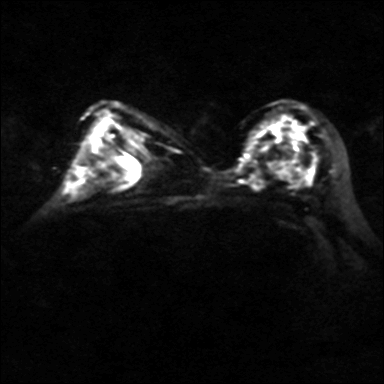
Breast MRI, one axial slice; position 24 of 40 along the scan axis; diffusion-weighted series; image 2 of 4 stored at this slice position (different b-values; order by instance number); 3 T; 4 mm slice thickness; 384 × 384 image matrix, field of view 320 × 320 mm. Female patient.
Structures marked on this image (outlined manually by an expert reader):
- tumour on diffusion-weighted imaging: bounding box [x1, y1, x2, y2] px = [280, 123, 305, 175]